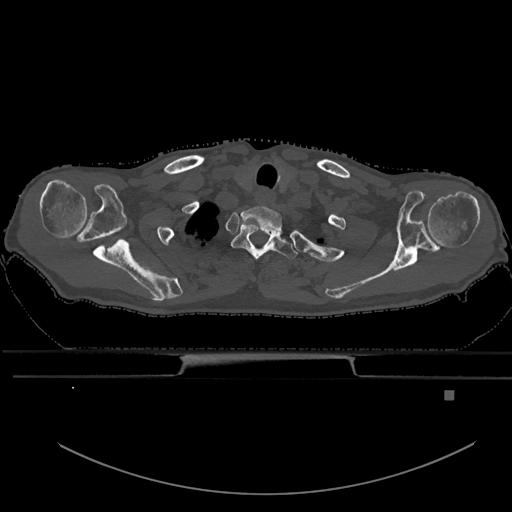
CT including the spine, one axial slice; slice 544 of 969 in the series (ordered by position); bone window (W 1800 / L 400 HU); 0.5 mm slice thickness; 512 × 512 image matrix, field of view 456 × 456 mm. Male patient, age 82 years. Case-level facts recorded for this patient, not image findings: primary cancer: prostate.
Outlined on this slice (semi-automatically segmented with operator editing):
- T1 vertebra: bounding box (x1, y1, x2, y2) in pixels: (231, 225, 298, 261)